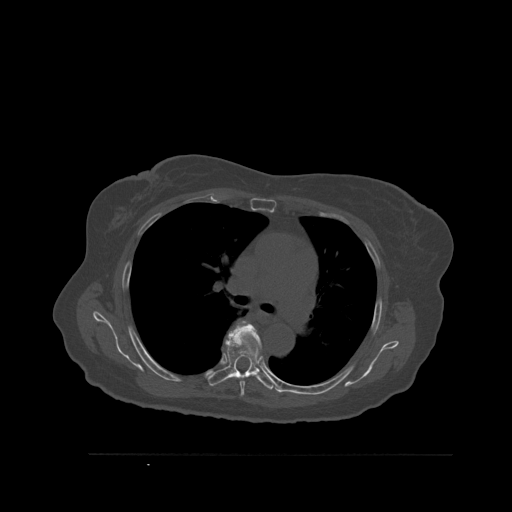
CT including the spine, one axial slice; position 386 of 527 along the scan axis; bone window (W 1800 / L 400 HU); 1.5 mm slice thickness; 512 × 512 image matrix, field of view 470 × 470 mm. Patient: female, 73 years. From the clinical record (not read from this slice): primary cancer: breast; vertebrae with lytic lesions (as recorded): L2.
Outlined on this slice (semi-automatically segmented with operator editing):
- T5 vertebra: bounding box [x1, y1, x2, y2] px = [240, 325, 262, 397]
- T6 vertebra: [207, 321, 275, 390]